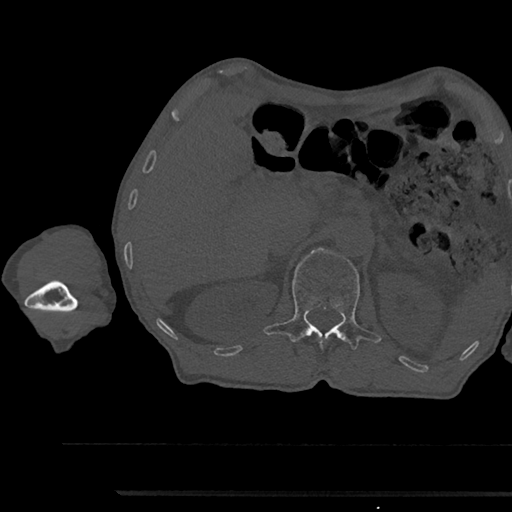
CT including the spine, one axial slice; position 648 of 797 along the scan axis; reconstruction kernel Br40s/3; bone window (W 1800 / L 400 HU); 0.5 mm slice thickness; 512 × 512 image matrix, field of view 367 × 367 mm. Patient: male, 79 years. Case-level facts recorded for this patient, not image findings: primary cancer: prostate.
Outlined on this slice (semi-automatic segmentation, software-assisted and operator-edited):
- L1 vertebra: bounding box <264,248,381,350> (left, top, right, bottom; pixels)